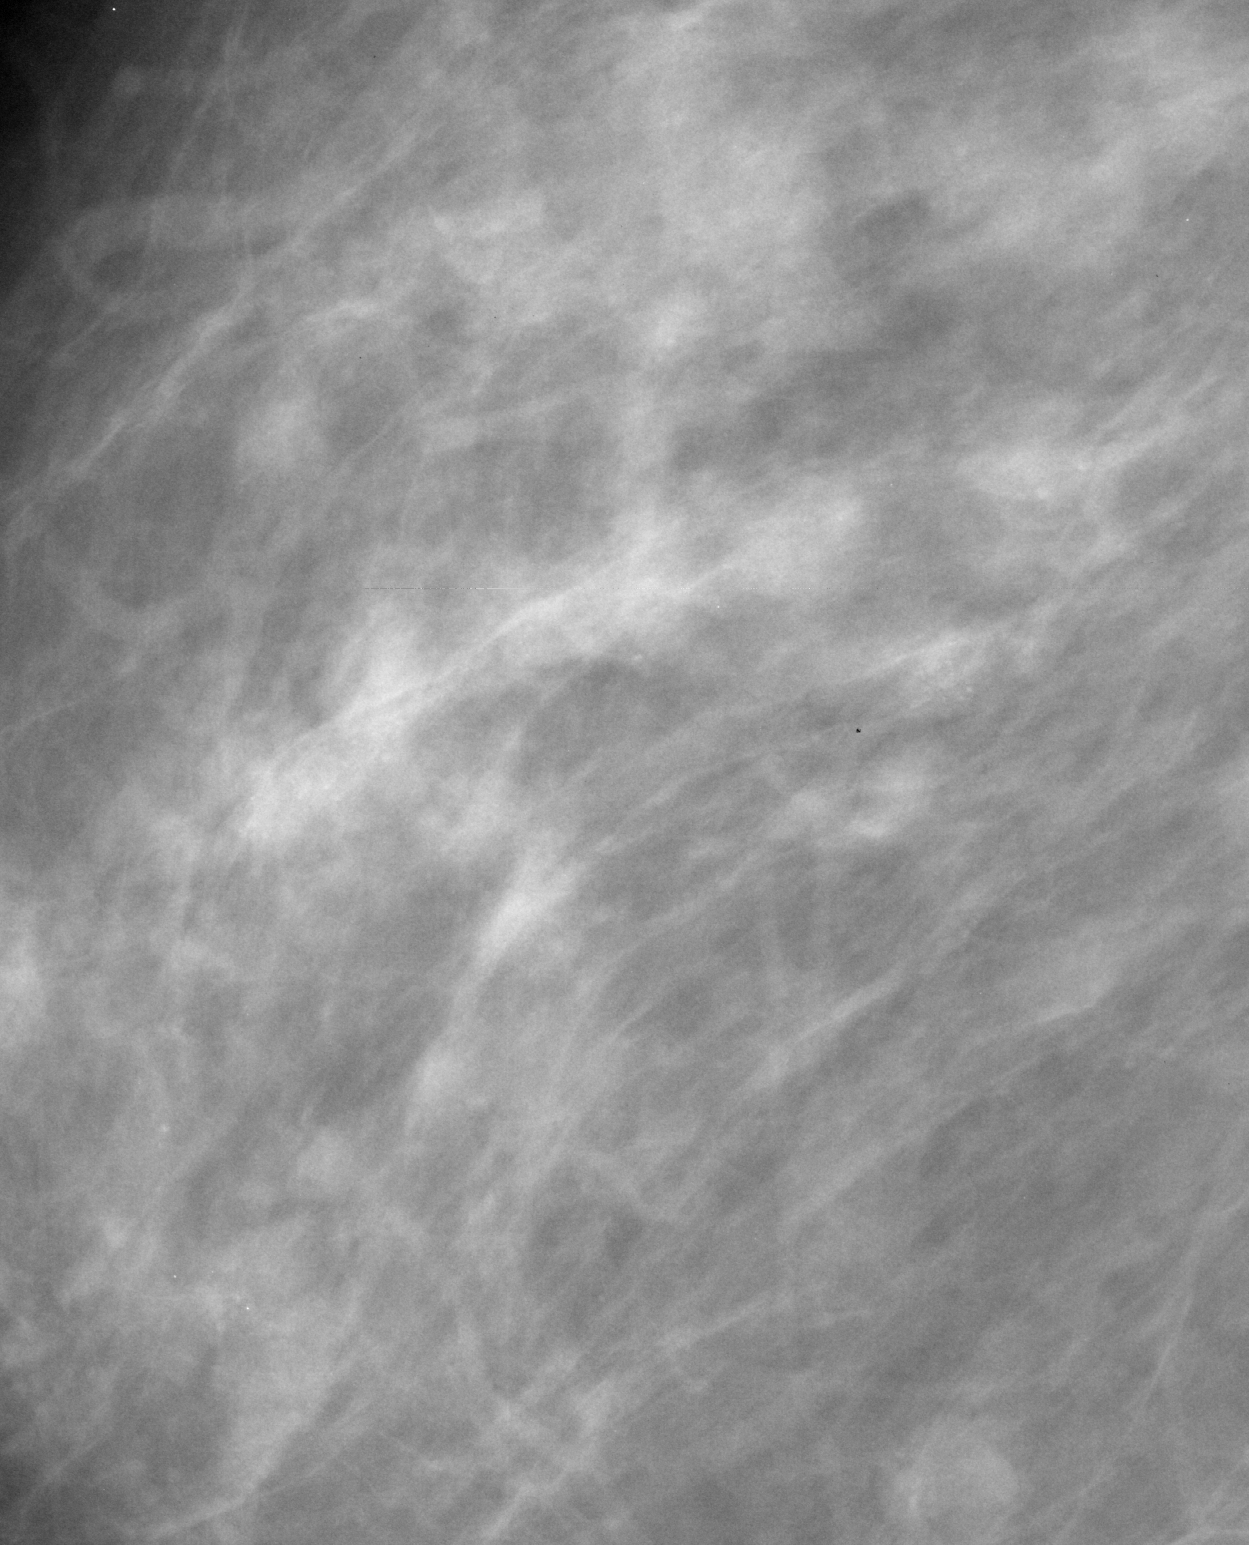
Cropped region of a digitized screen-film mammogram centred on a radiologist-marked abnormality; right breast; MLO view.
Finding: calcifications, morphology amorphous, distribution regional; BI-RADS assessment category 4; pathology (as recorded): benign.